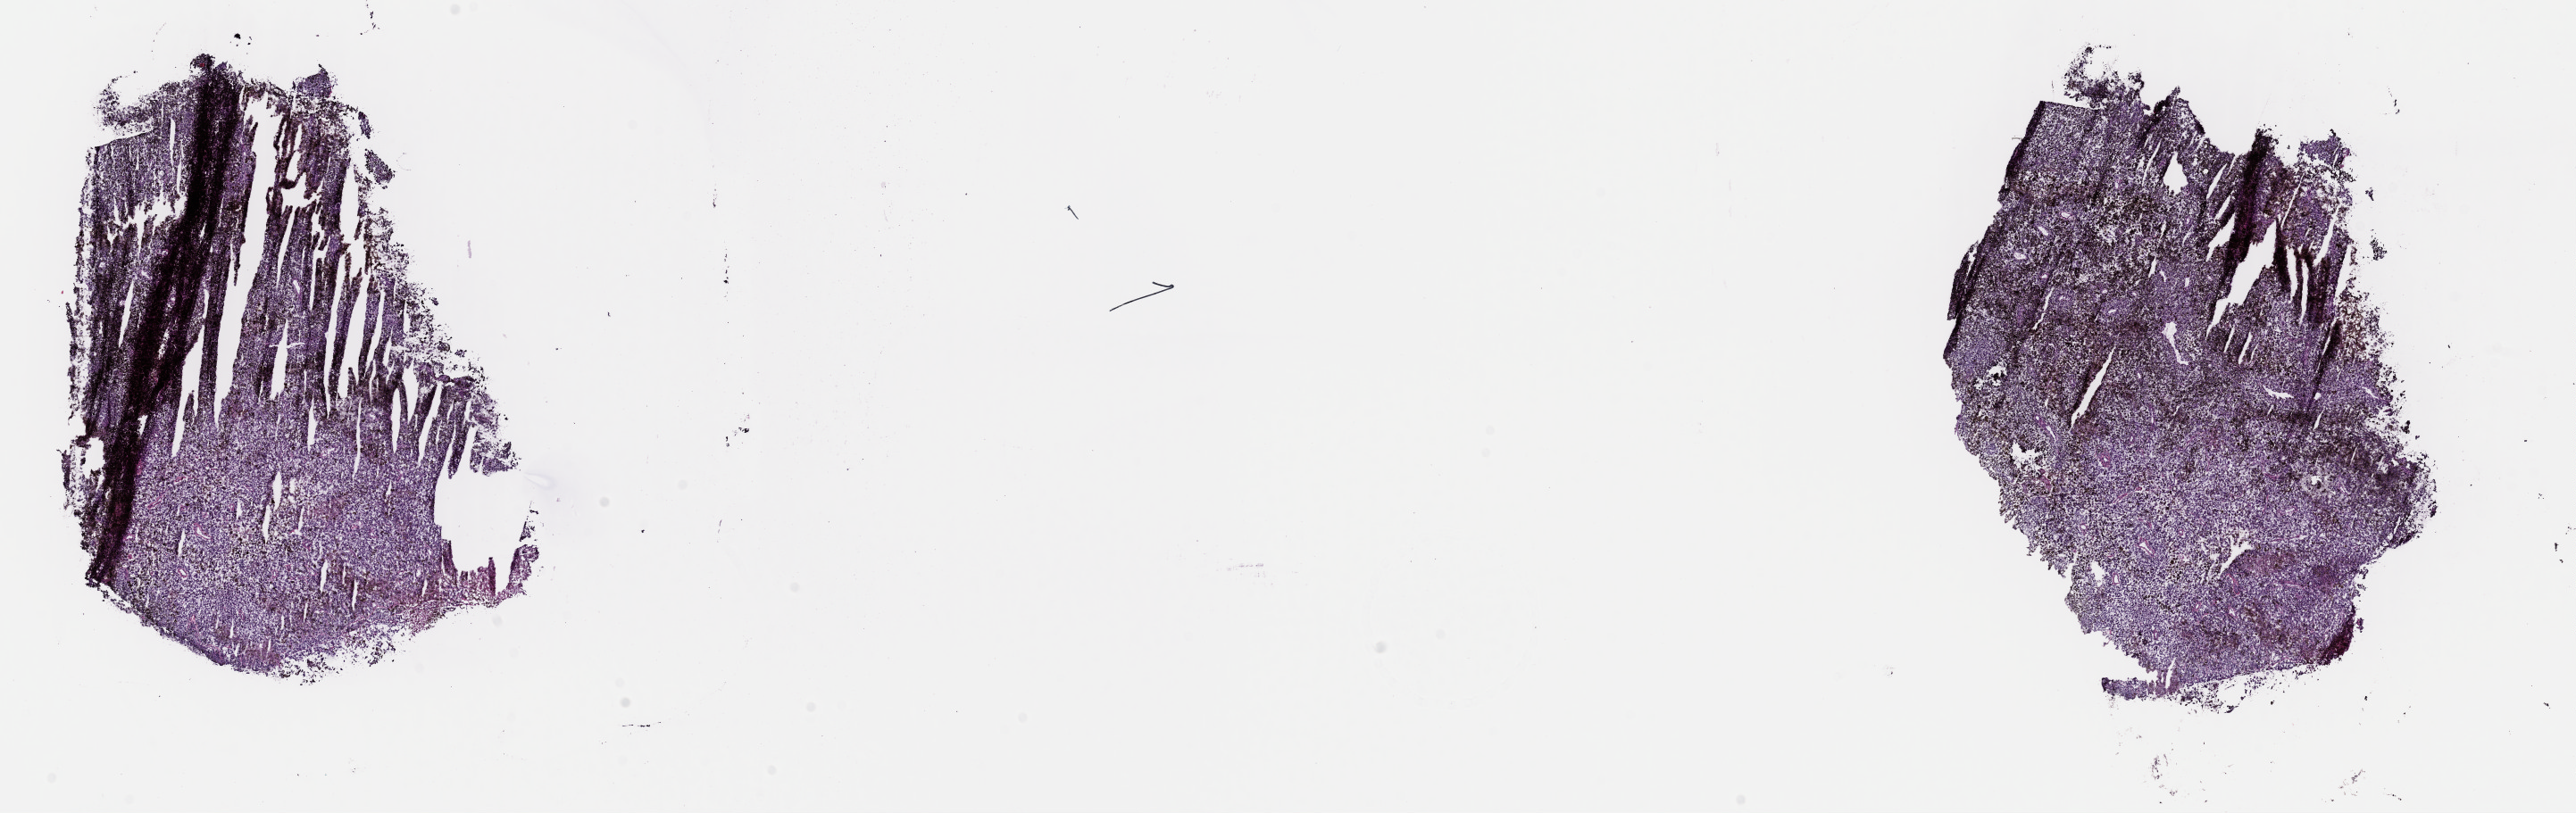
Hematoxylin and eosin (H&E) stained whole-slide image — whole scanned area (about 22.8 x 7.2 mm, acquisition: 40x scan) shown as a low-resolution overview, frozen section from the top of the tissue portion, metastatic tumour sample, sampled site: lung. Male, age 31 years at initial diagnosis. Pathologist review of this section (percent, as recorded): tumour cells 100%, tumour nuclei 96%, normal cells 0%, stromal cells 0%, necrosis 0%. Inflammatory infiltration, as recorded: lymphocyte infiltration 0%, monocyte infiltration 0%, neutrophil infiltration 0%.
This section: metastatic tumour tissue. Patient diagnosis: Malignant melanoma, NOS.